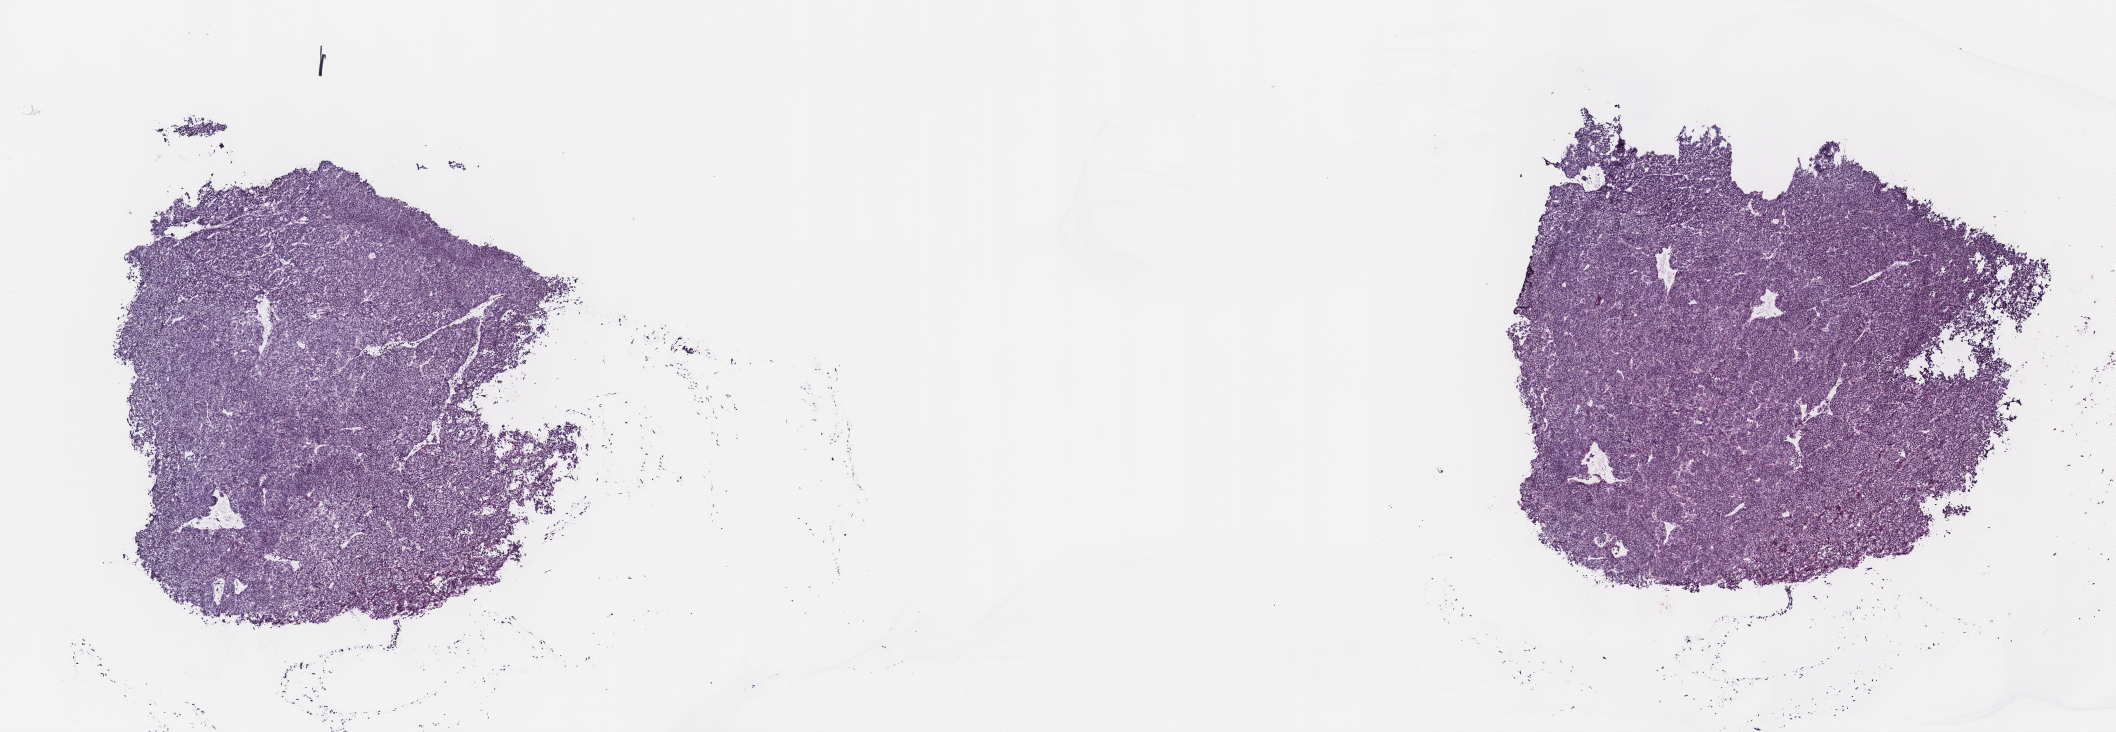
Whole-slide histology image, Hematoxylin and eosin (H&E) stained, shown as a low-resolution overview of the whole scanned area (about 17.1 x 5.9 mm, slide scanned at 40x); frozen section from the top of the tissue portion; uvea, primary tumour sample. Male, age 75 years at initial diagnosis. Composition of this section per pathologist review: tumour cells 85%, tumour nuclei 85%.
Pathologic diagnosis: Mixed epithelioid and spindle cell melanoma (choroid).